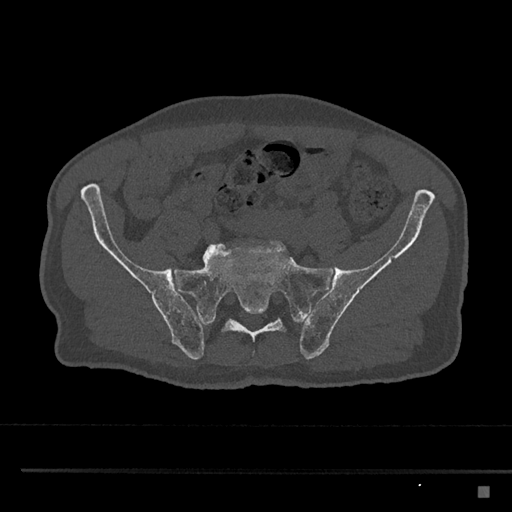
CT including the spine, one axial slice. Reconstruction kernel Br40s/3. Bone window (W 1800 / L 400 HU). 0.5 mm slice thickness. 512 × 512 image matrix. Patient: male, 59 years. Case-level facts recorded for this patient, not image findings: primary cancer: prostate.
Outlined on this slice (semi-automatically segmented with operator editing):
- L5 vertebra: box from (x=202, y=244) to (x=266, y=262) px